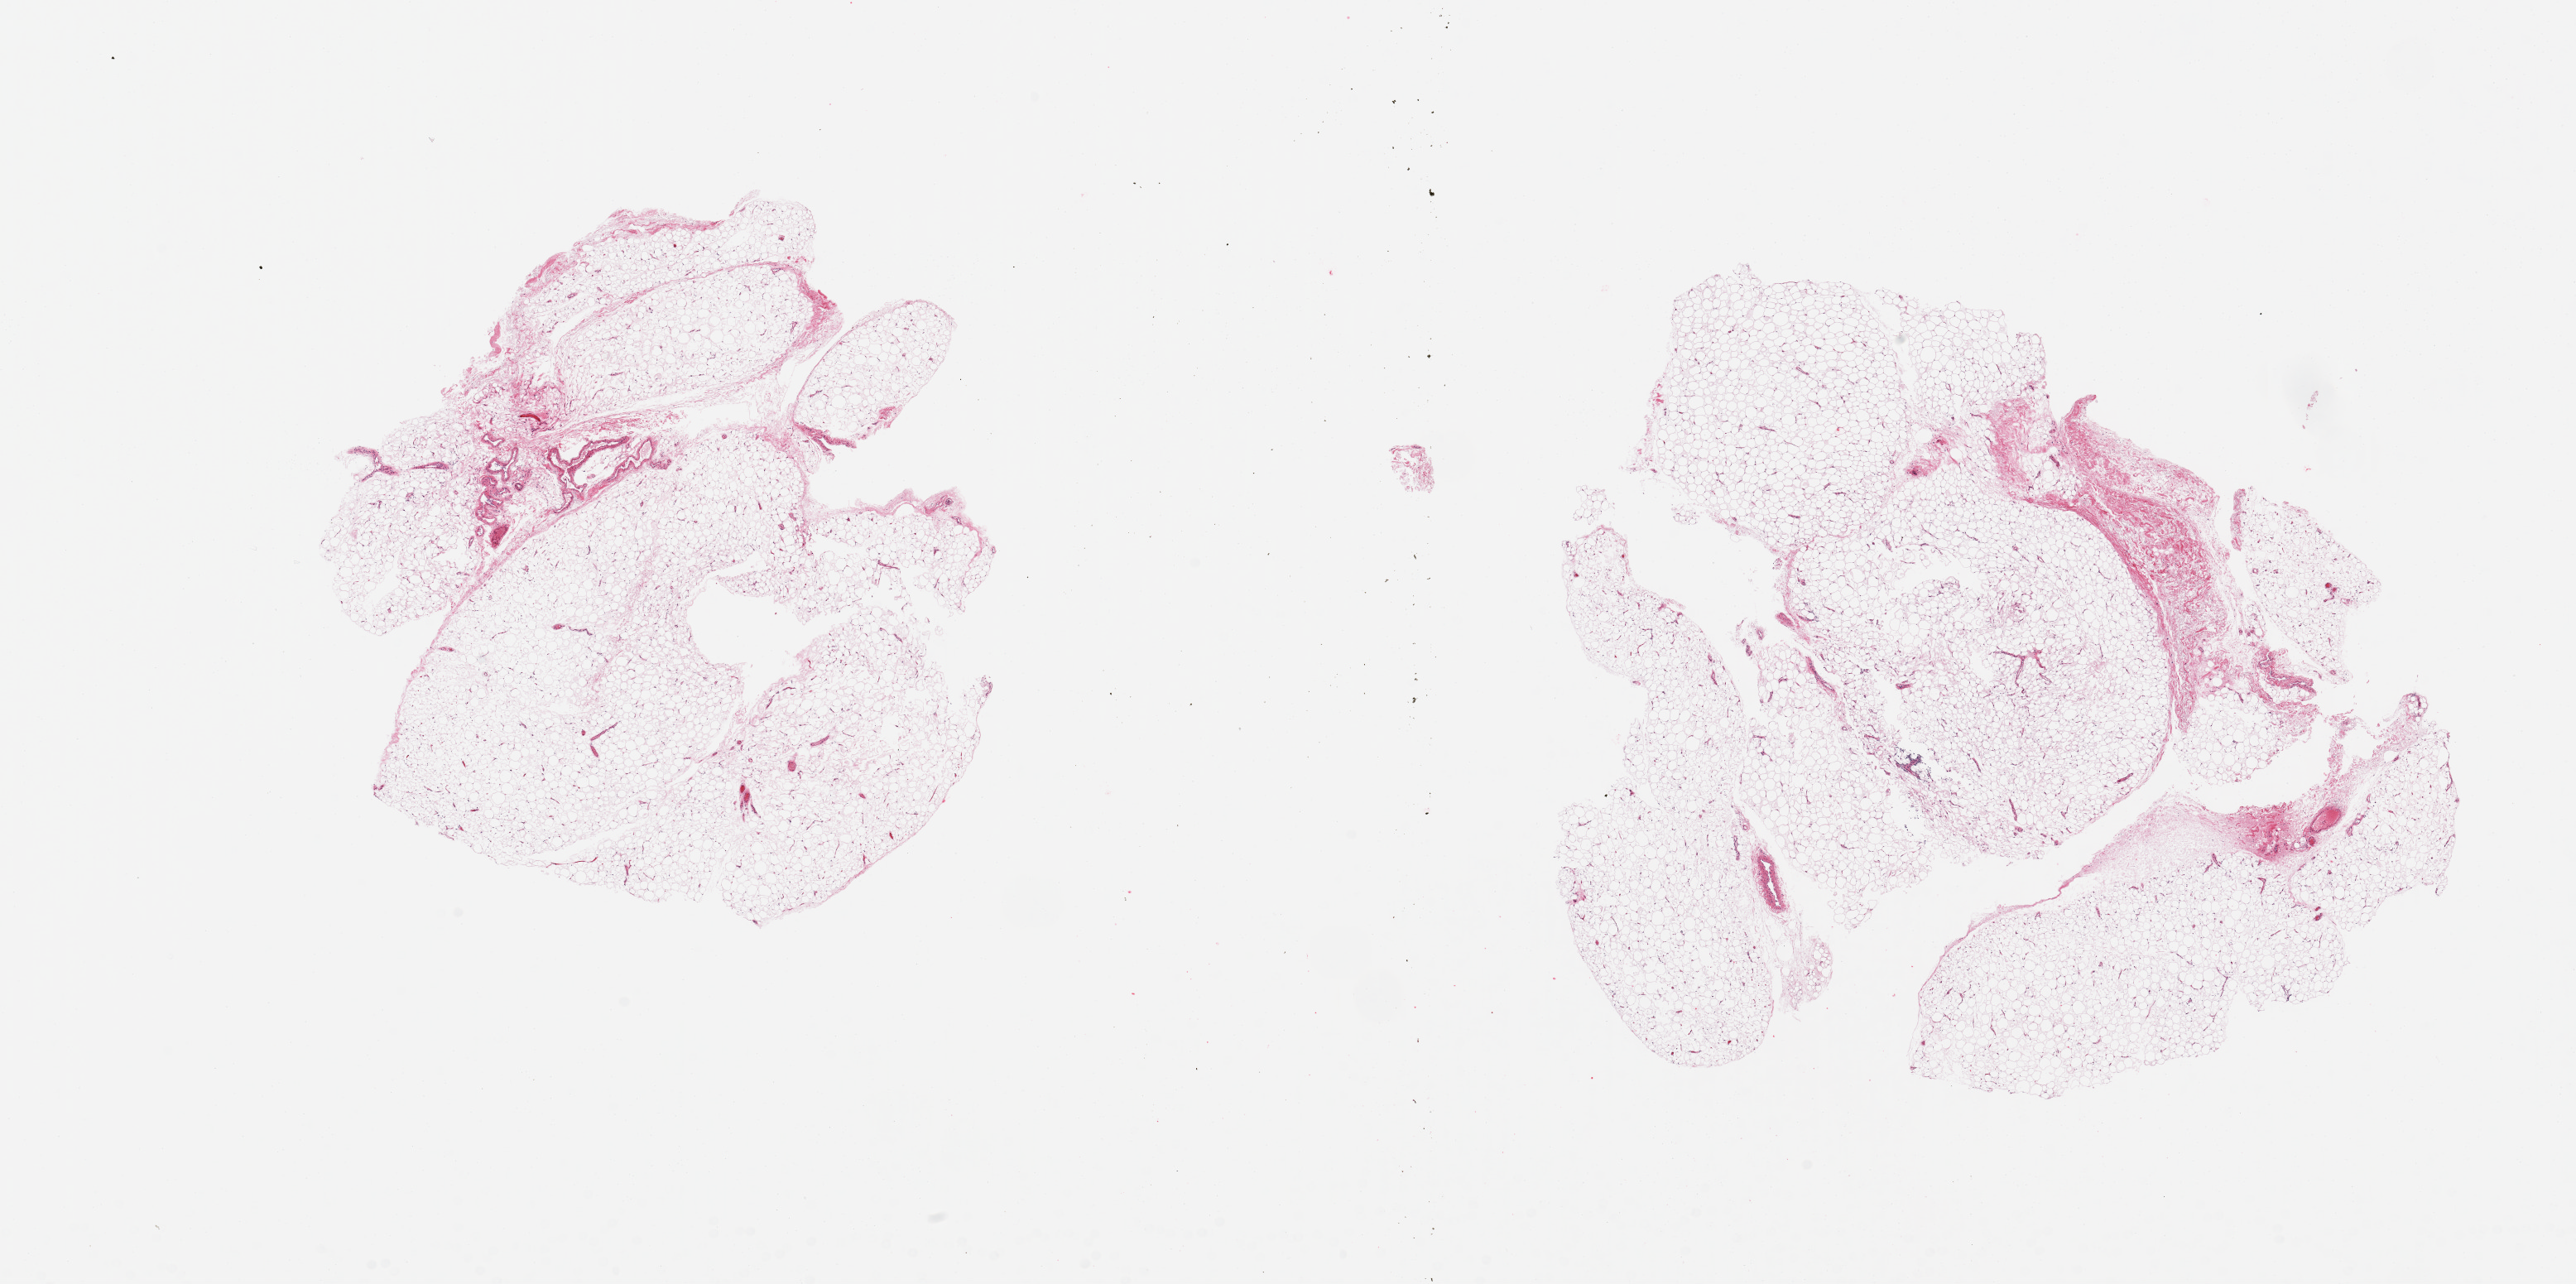
Haematoxylin and eosin whole-slide image, shown as a low-resolution overview of the whole scanned area (about 24.6 x 12.3 mm, slide scanned at 20x). PAXgene-fixed paraffin-embedded (PFPE) section. Target tissue: adipose tissue. Tissue donor sample. Male donor.
* reviewer comment on this tissue sample: 2 pieces; mature adipose tissue and fibrovascular component (~5%)